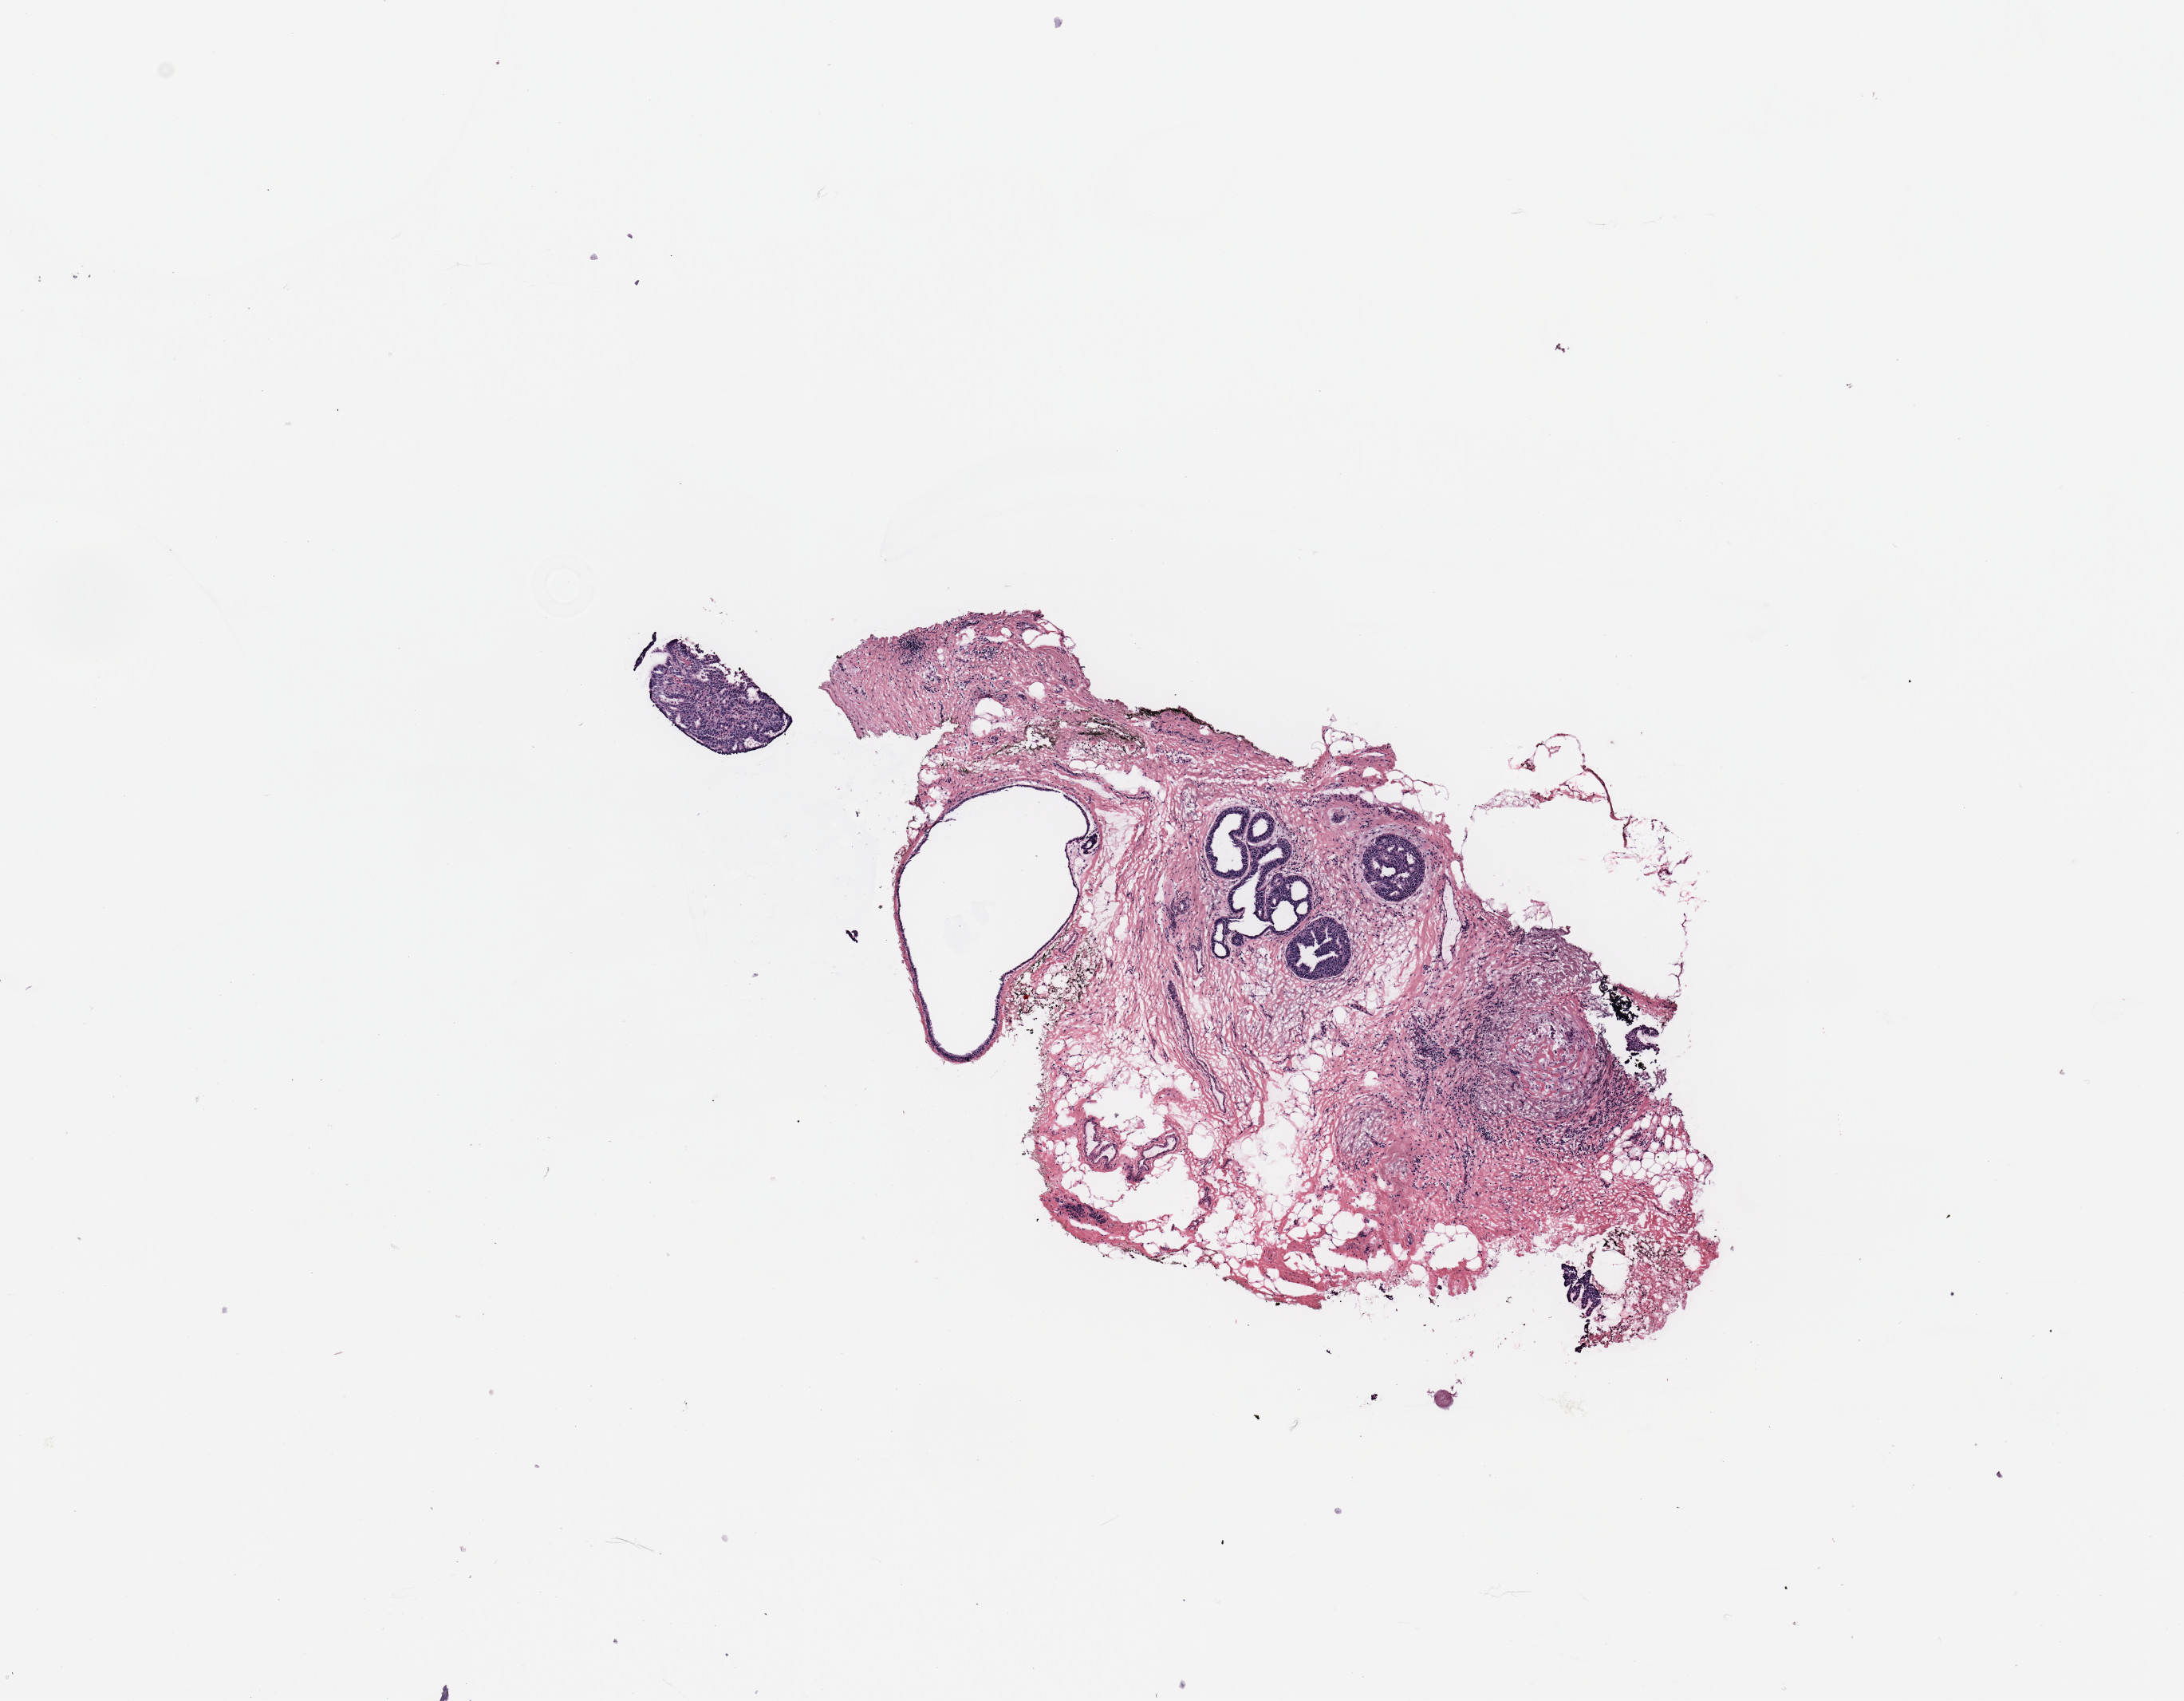
Whole-slide histology image, H&E — a low-resolution overview of the entire scanned area, about 10.8 x 8.4 mm; breast, tissue type not recorded. 46-year-old female patient.
Patient diagnosis: Infiltrating duct carcinoma, NOS.